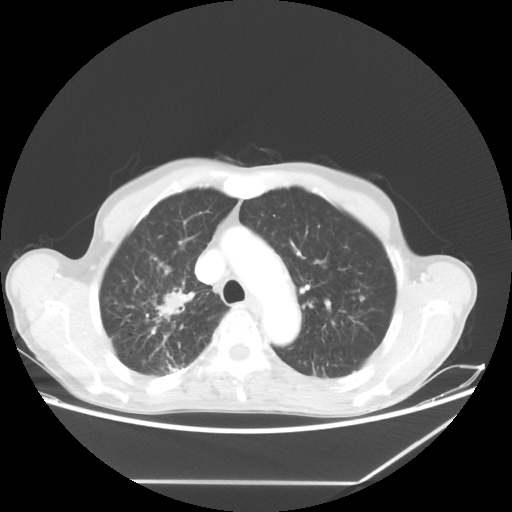
Chest CT, one axial slice; slice 47 of 65 in the series (ordered by position); reconstruction kernel STANDARD; 80 kVp; lung window (W 1500 / L -600 HU); 512 × 512 image matrix, field of view 397 × 397 mm. Male patient, age 68 years. From the clinical record (not read from this slice): clinical TNM (as recorded): T3 N3 M0.
Structures marked on this image (rectangle marked by the reading radiologist):
- lung tumour (recorded histology: adenocarcinoma): bounding box (x1, y1, x2, y2) in pixels: (150, 285, 198, 328)